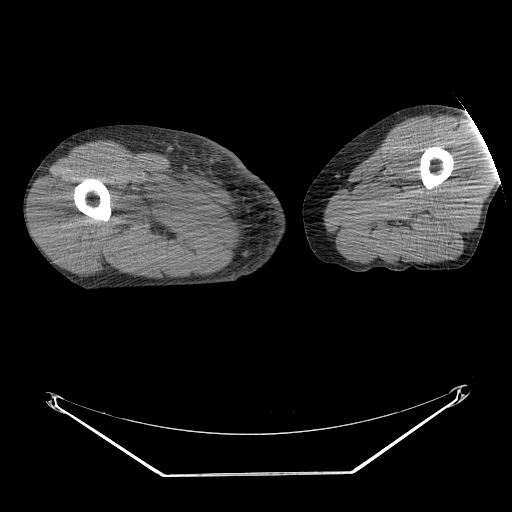
CT of an extremity soft-tissue mass (from a PET/CT study), one axial slice; position 237 of 311 along the scan axis; reconstruction kernel STANDARD; 140 kVp; soft-tissue window (W 400 / L 40 HU); 3.75 mm slice thickness; 512 × 512 image matrix. Male patient. From the clinical record (not read from this slice): histological type: undifferentiated - pleiomorphic; grade: high; site of the primary tumour: right thigh.
Outlined on this slice (expert contour drawn on MRI and transferred to this co-registered scan by the dataset authors):
- gross tumour volume including surrounding oedema: bounding box <133,185,206,223> (left, top, right, bottom; pixels)